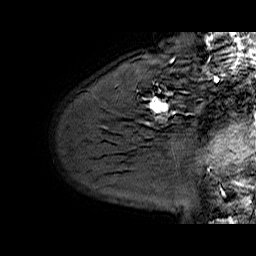
Breast MRI (dynamic contrast-enhanced), one sagittal slice. Dynamic contrast-enhanced series, time point 2 of 6 at this slice position (early post-contrast). 1.5 T. TE 6.4 ms, TR 32.9 ms. 4 mm slice thickness. 256 × 256 image matrix, field of view 200 × 200 mm. Female patient. From the clinical record (not read from this slice): setting: breast cancer imaged before/during neoadjuvant chemotherapy; receptor status: HER2-positive.
Outlined on this slice (semi-automatically segmented with operator editing):
- analysis volume of interest (the breast-tissue region the enhancement analysis was run in; not a lesion): bounding box [x1, y1, x2, y2] px = [130, 62, 202, 128]
- tumour enhancement mask (voxels above the 100 % enhancement threshold inside the analysis volume of interest): [150, 93, 172, 118]